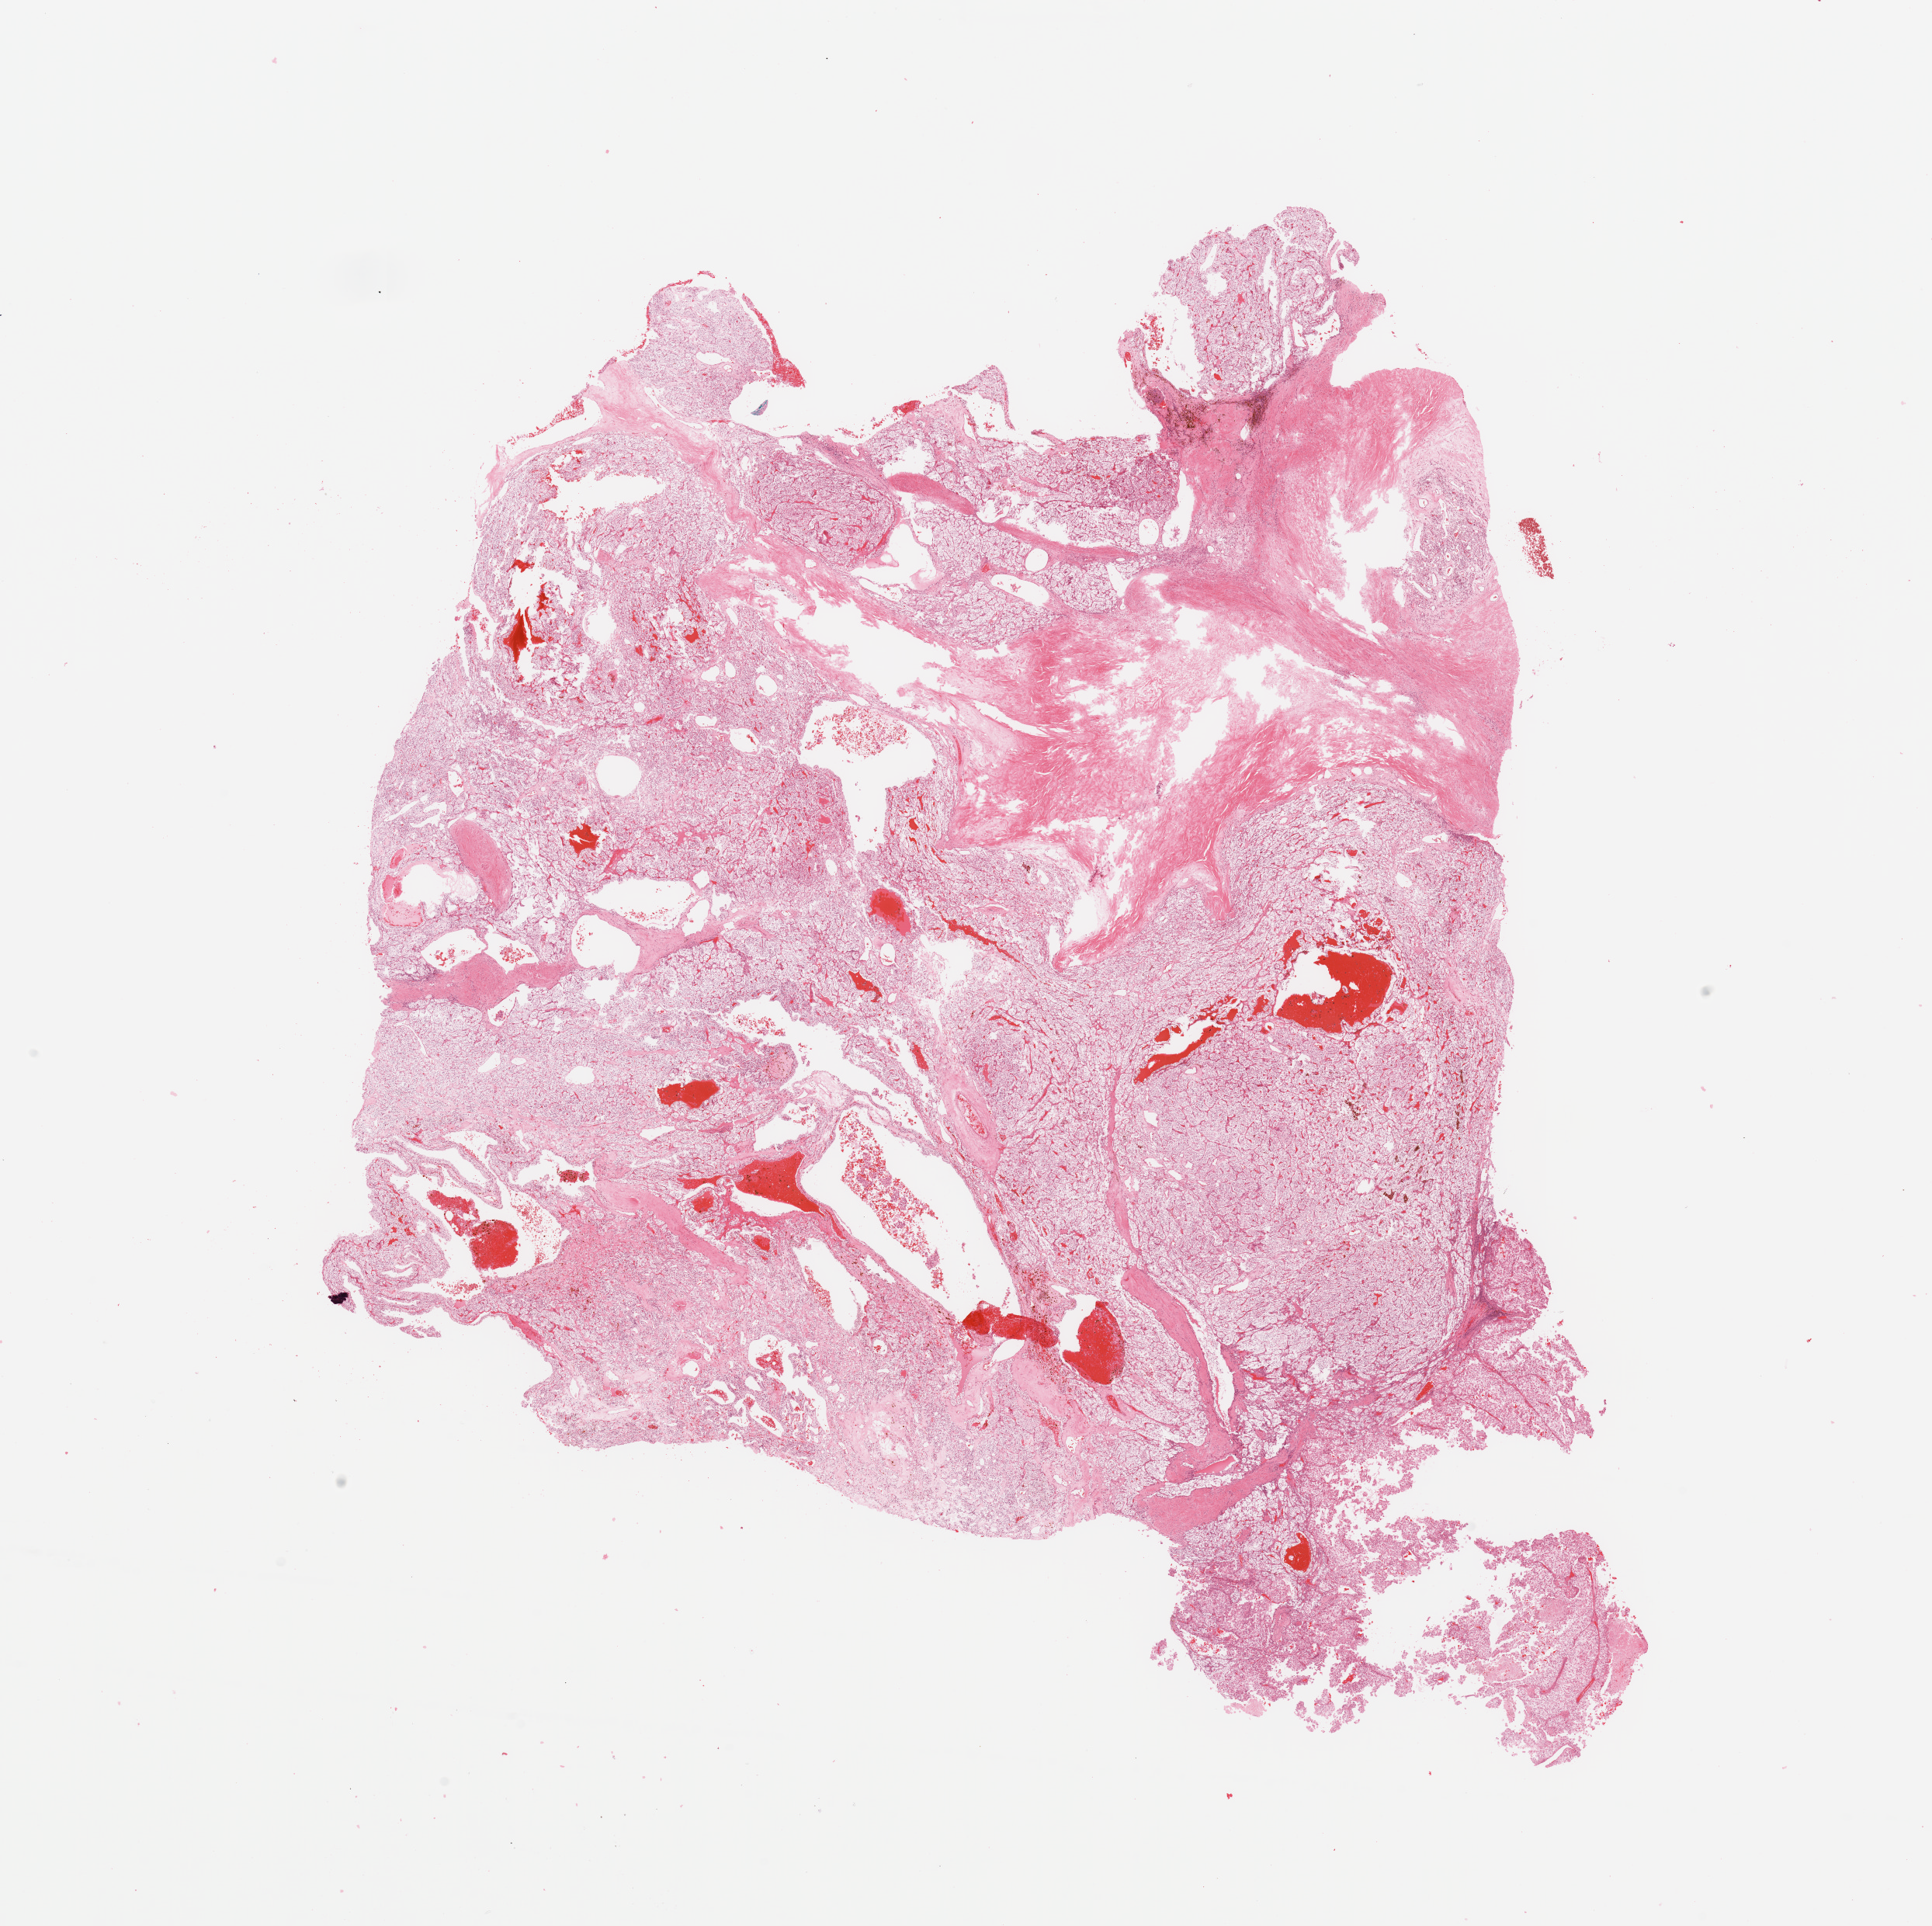
Hematoxylin and eosin (H&E) stained whole-slide image — shown as a low-resolution overview of the whole scanned area (about 19.7 x 19.6 mm, from a 20x scan); tumour tissue sample, sampled site: kidney. Patient: male, age 66 years. Histologic grade: G1 (well differentiated). Slide review estimates, as recorded: tumour nuclei 85%, necrosis 5%.
• diagnosis: Renal cell carcinoma, NOS